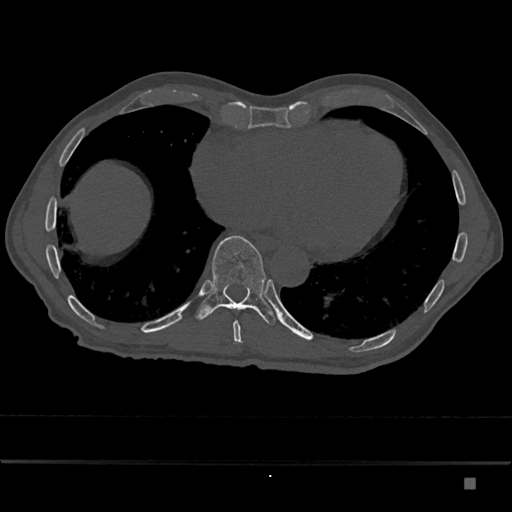
CT including the spine, one axial slice. Position 758 of 797 along the scan axis. Reconstruction kernel Br40s/3. 120 kVp. Bone window (W 1800 / L 400 HU). 0.5 mm slice thickness. 512 × 512 image matrix, field of view 390 × 390 mm. Patient: male, 72 years. Case-level facts recorded for this patient, not image findings: primary cancer: prostate.
Structures marked on this image (semi-automatically segmented with operator editing):
- T10 vertebra: bounding box (x1, y1, x2, y2) in pixels: (195, 235, 276, 326)
- T9 vertebra: (233, 321, 243, 344)